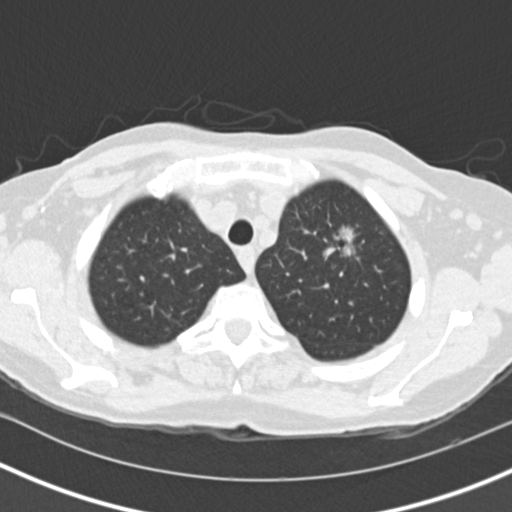
Low-dose screening chest CT, one axial slice; position 122 of 146 along the scan axis; lung window (W 1500 / L -600 HU); 2 mm slice thickness; 512 × 512 image matrix, field of view 310 × 310 mm.
Outlined on this slice (expert manual segmentation):
- lesion 1 (tumor, upper lobe of left lung): bounding box [x1, y1, x2, y2] px = [335, 227, 354, 256]